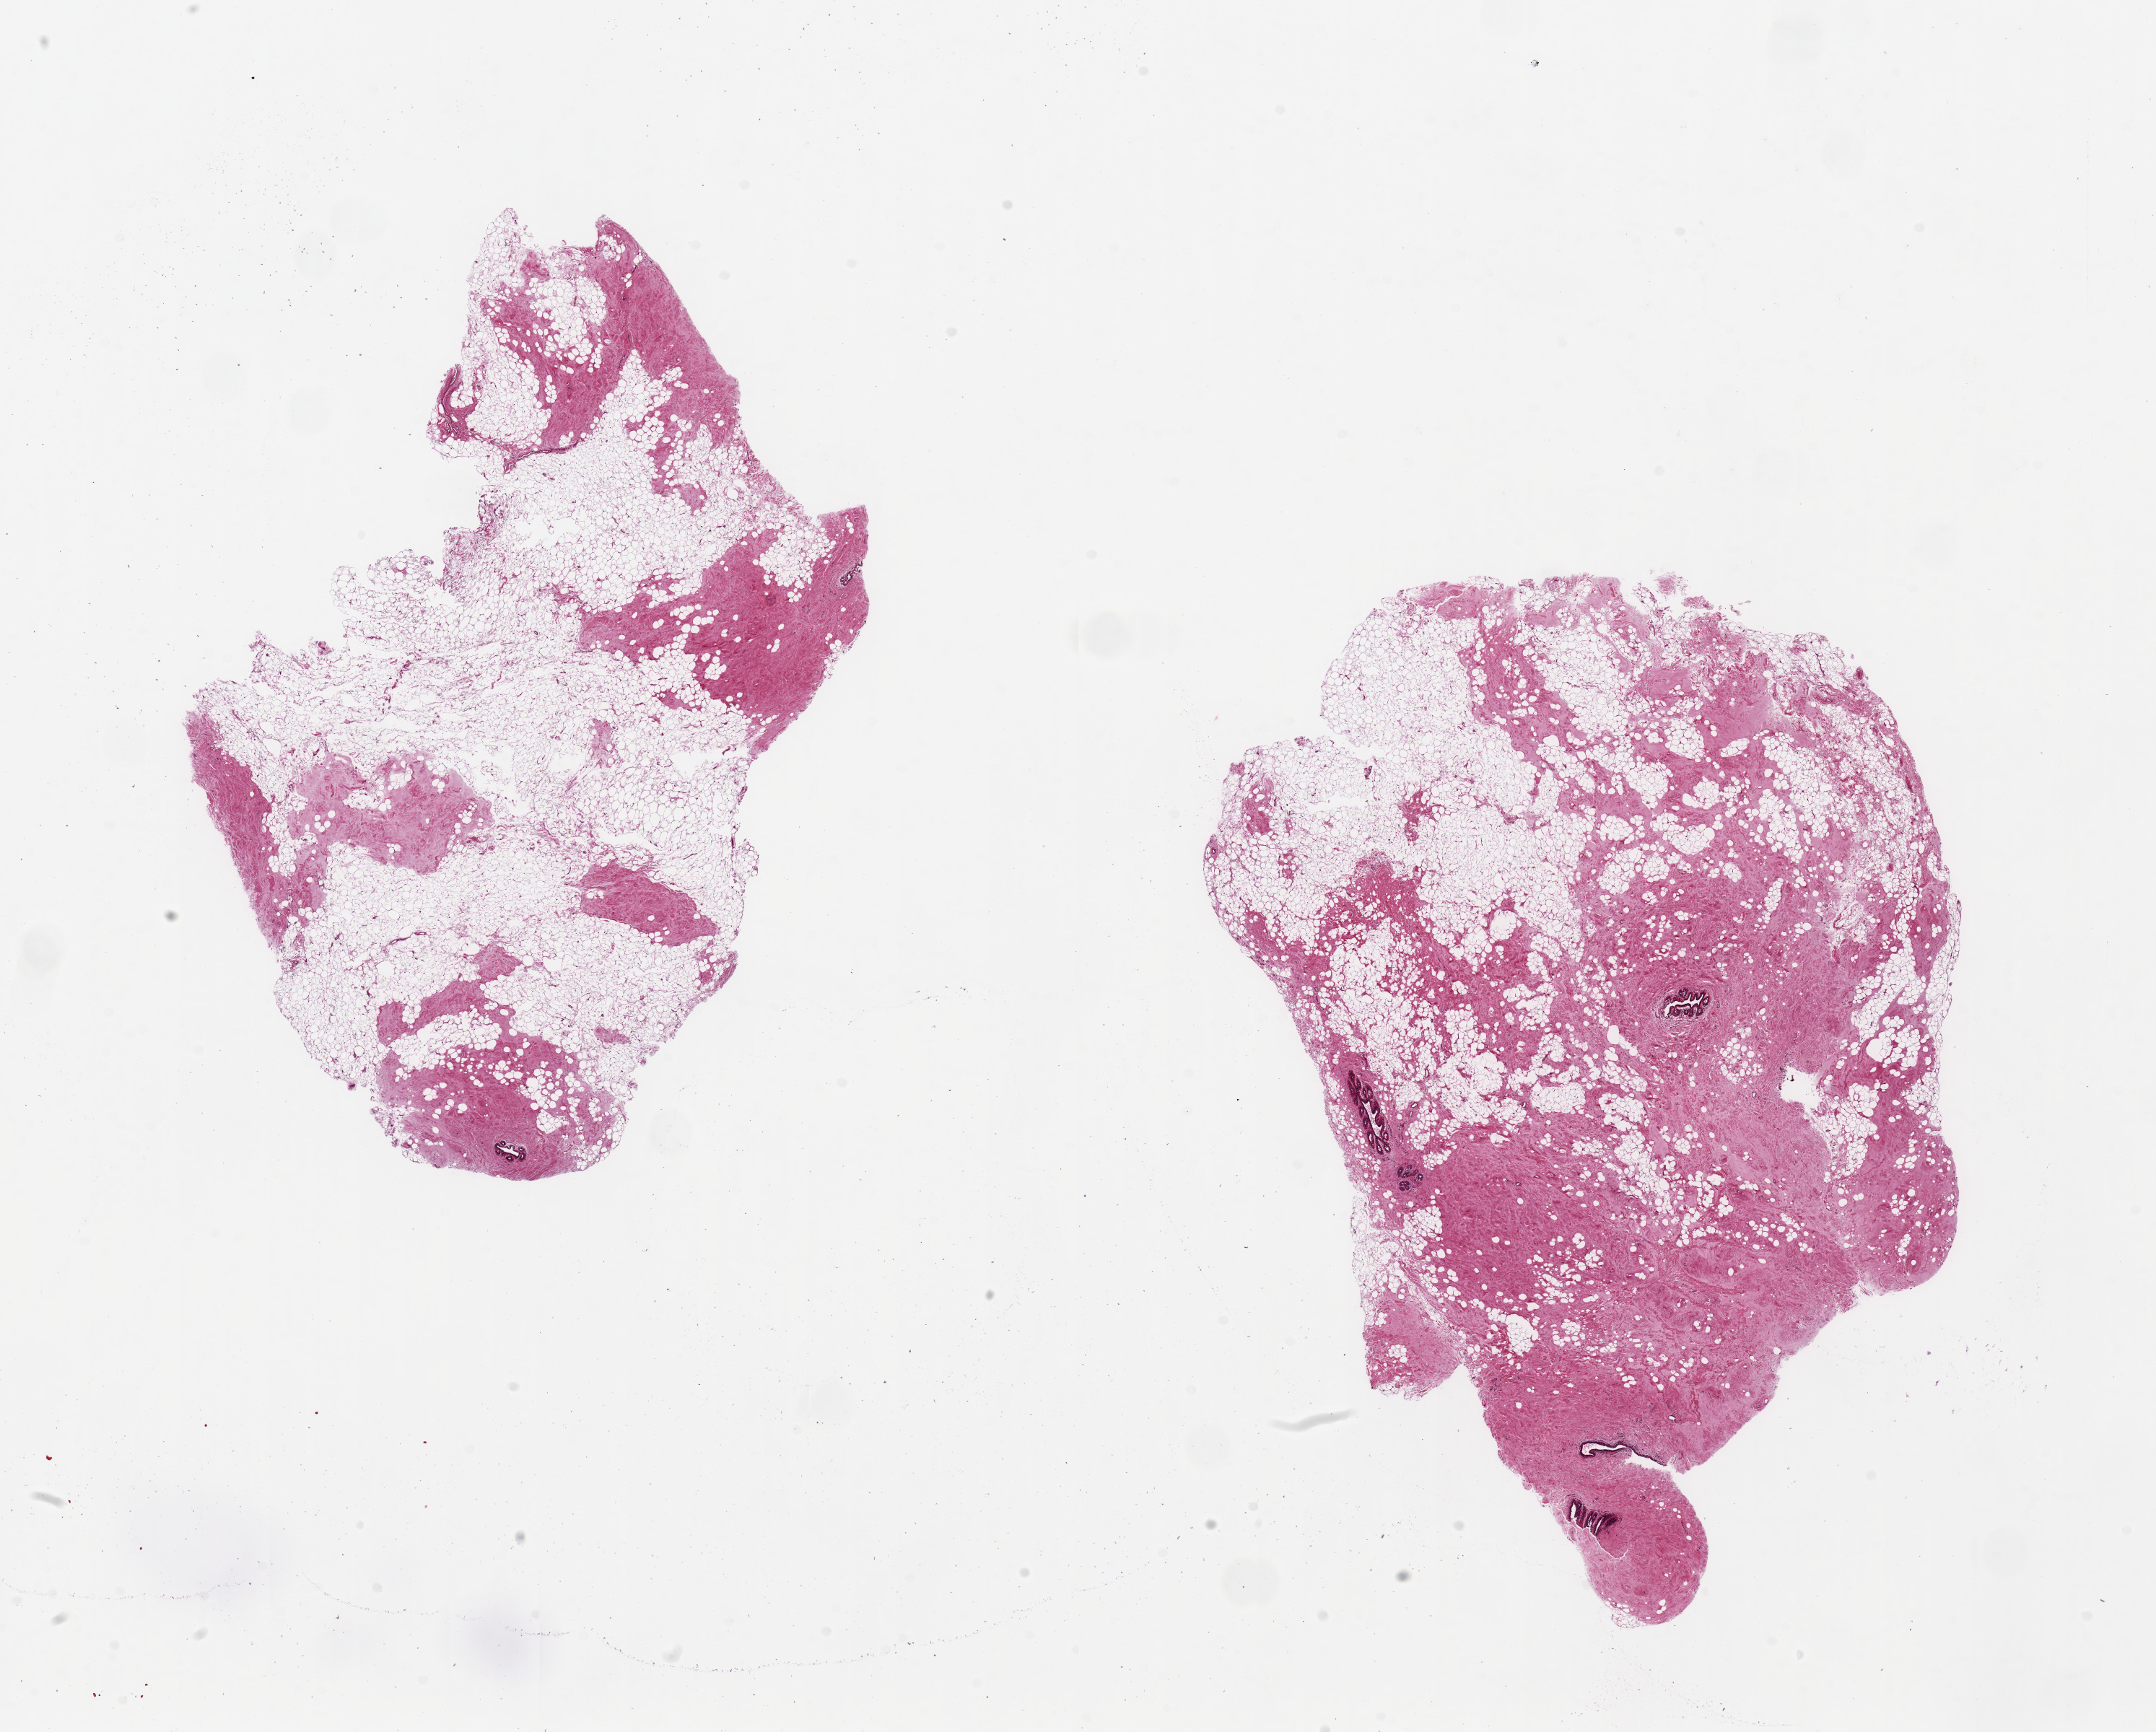
H&E whole-slide image, low-resolution overview of the scanned area, about 23.6 x 19.0 mm (slide scanned at 20x). PAXgene-fixed, paraffin-embedded tissue. Target tissue: breast. Tissue donor sample.
Review note (as recorded): 2 pieces, 10x8 & 11x8mm; mainly ducts; 50-80% adipose.